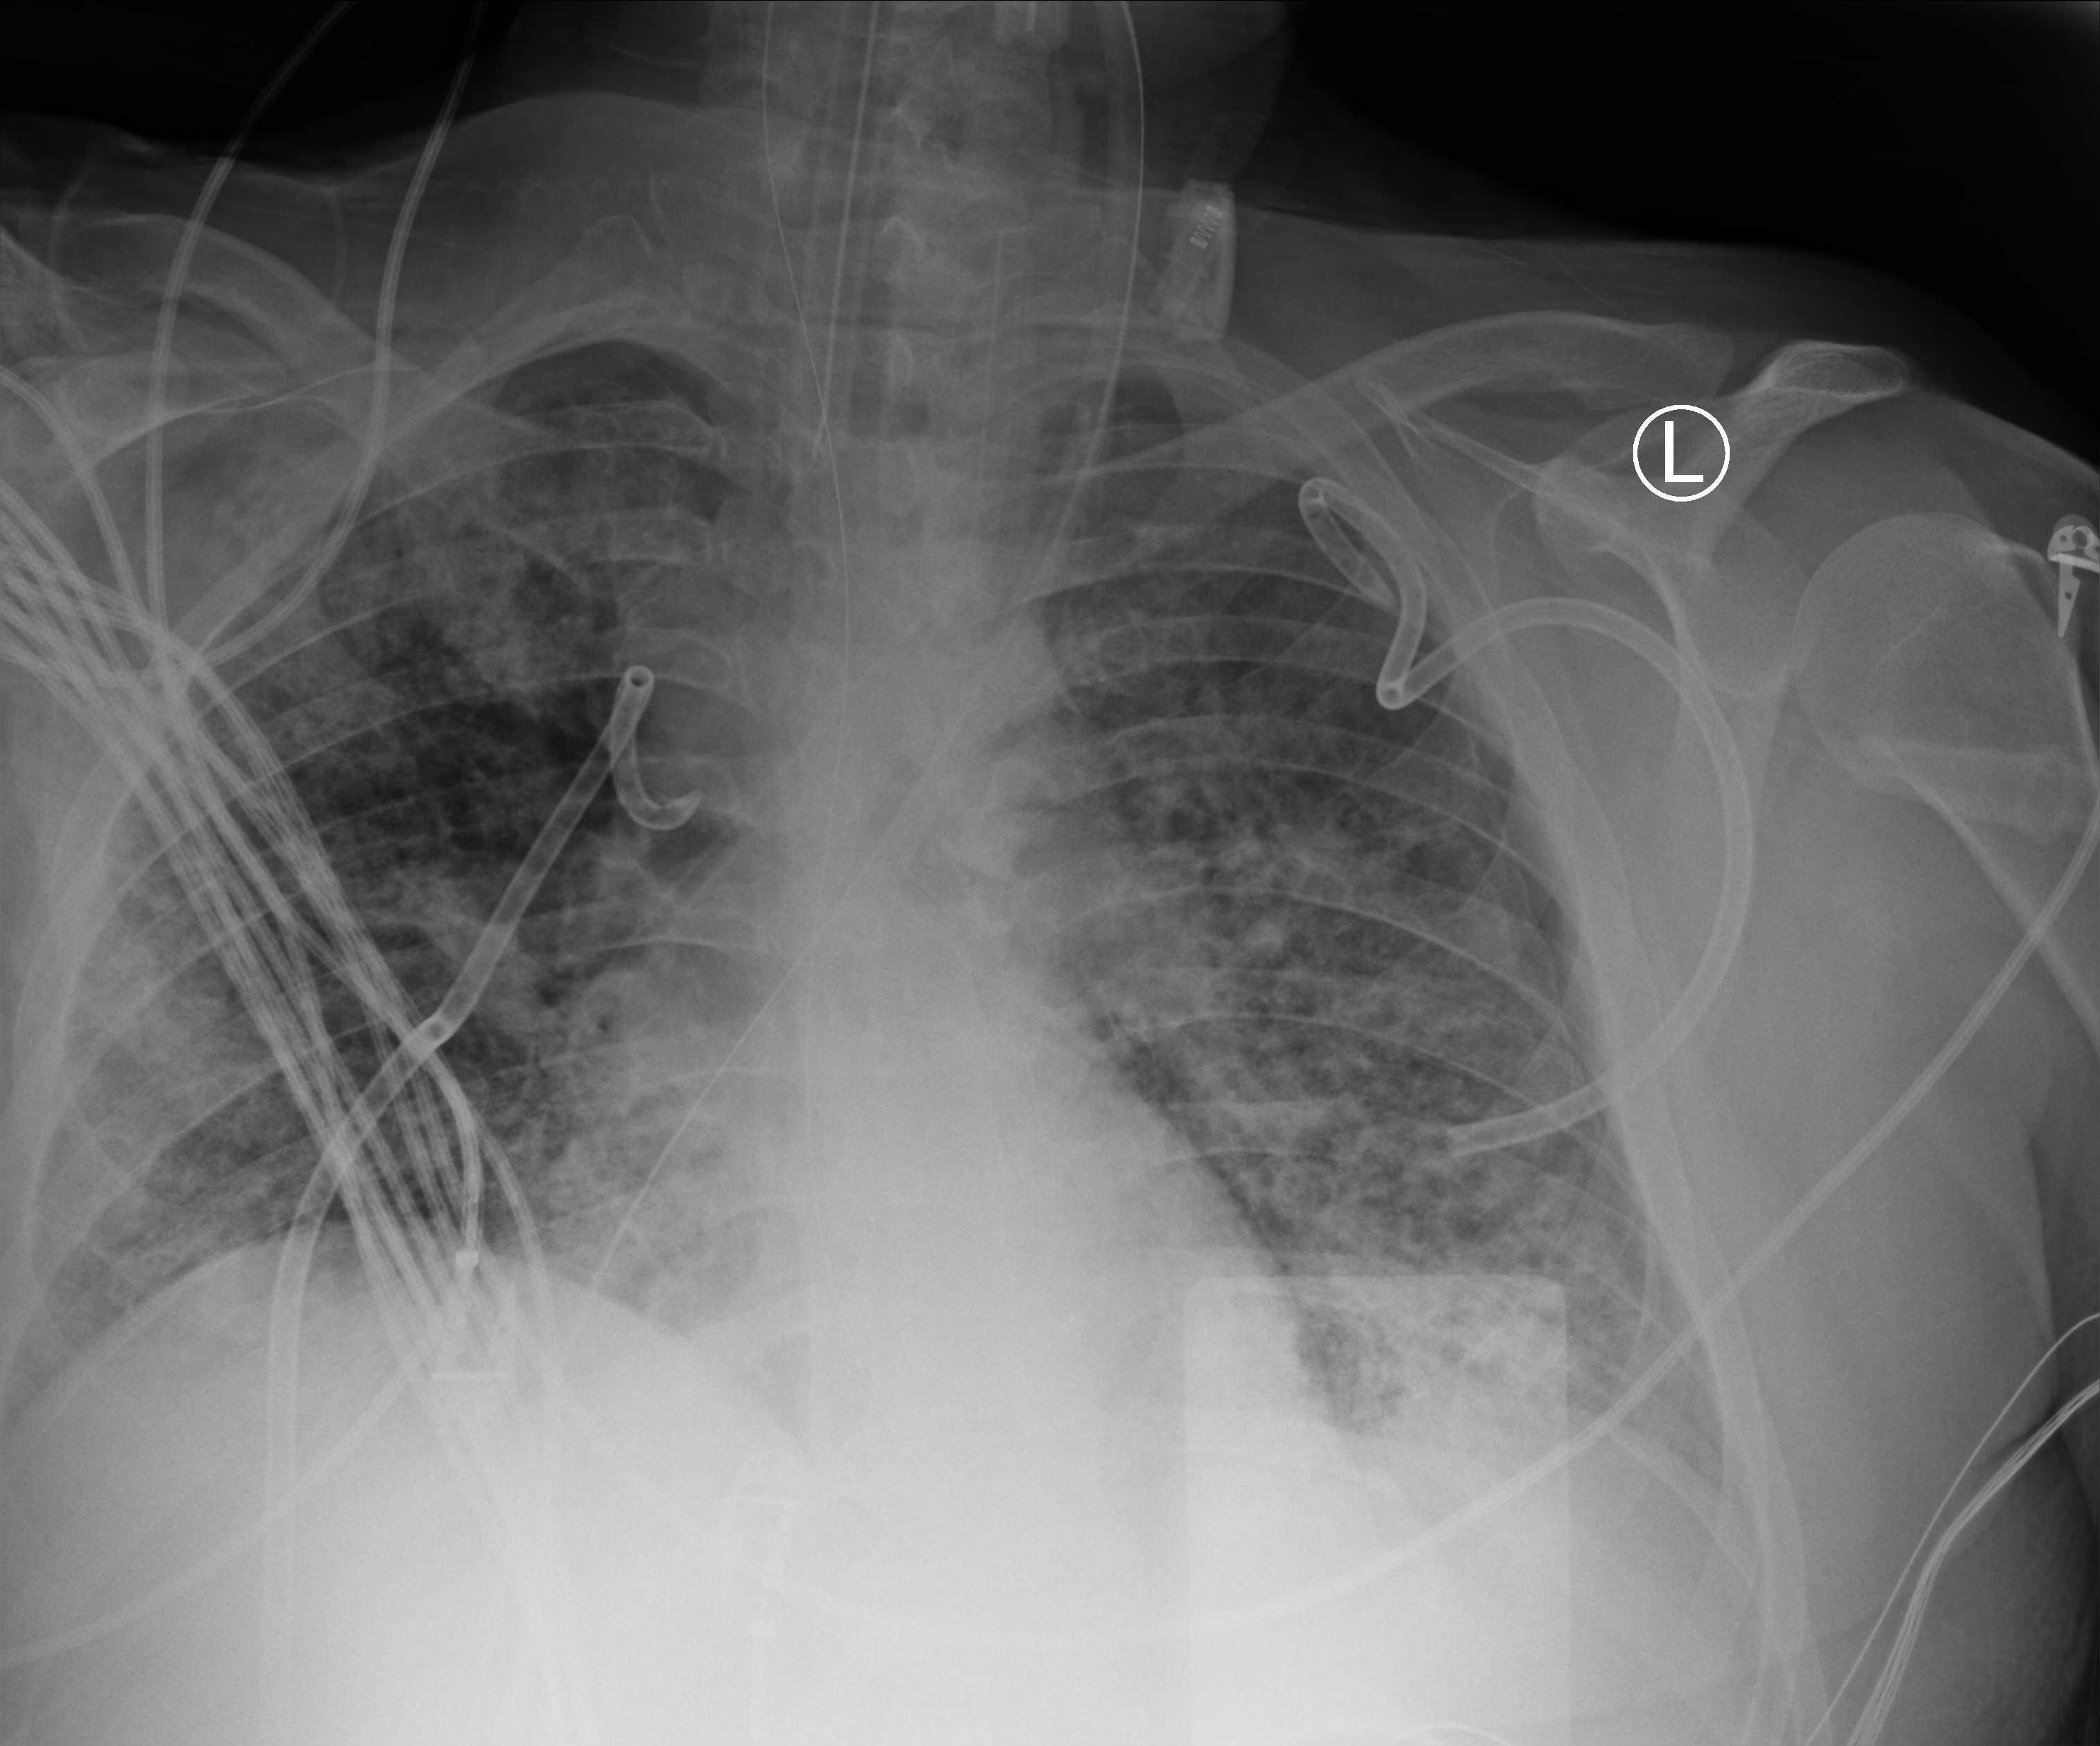
Chest X-ray (portable), anteroposterior (AP) projection. Adult patient hospitalised with COVID-19, age 18–59 years.
From the hospital-stay record, not from the radiograph (when in the stay this image was taken is not recorded):
- mechanically ventilated during this hospital stay: yes
- length of hospital stay: 31 days